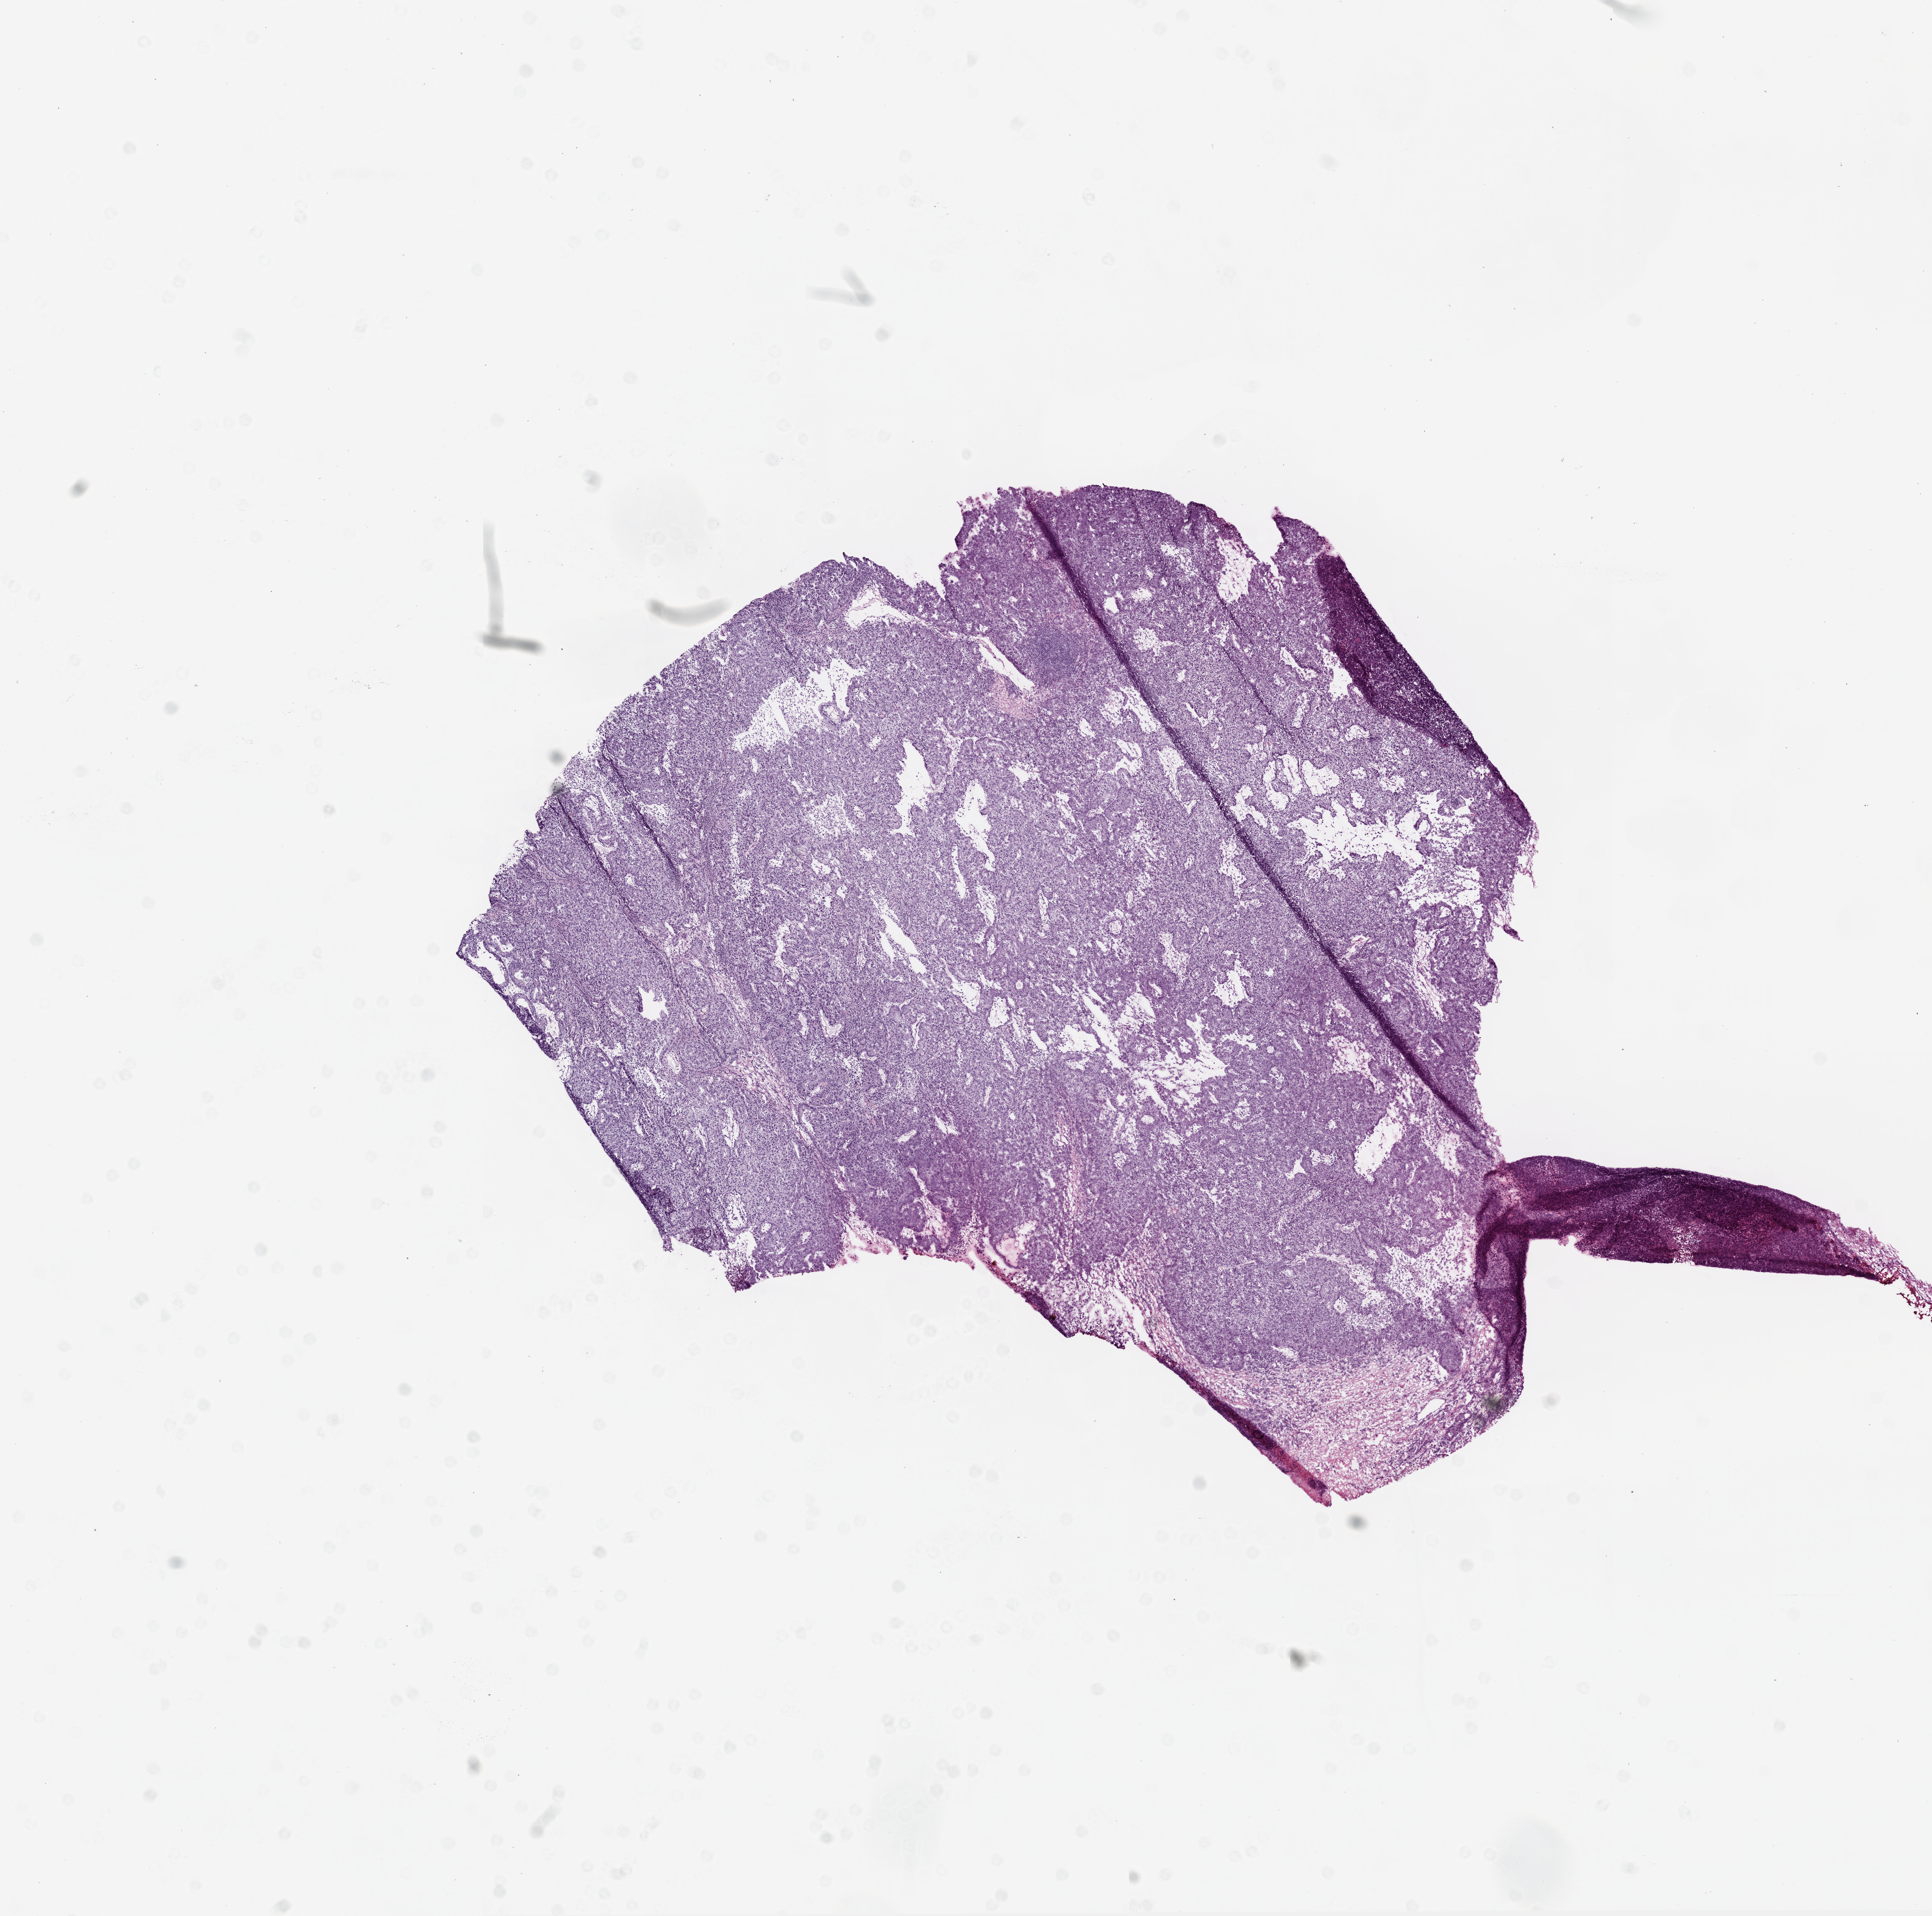
Digitized H&E-stained tissue section (whole slide) — low-resolution overview of the scanned area, about 12.0 x 11.9 mm. Frozen section from the top of the tissue portion. Lung, primary tumour sample. Male patient; age at initial diagnosis 68 years. Slide review estimates, as recorded: tumour cells 89%, tumour nuclei 70%, normal cells 0%, stromal cells 10%, necrosis 1%.
Diagnosis: Adenocarcinoma with mixed subtypes (lower lobe, lung). Laterality: left. AJCC pathologic stage: IB (6th edition).